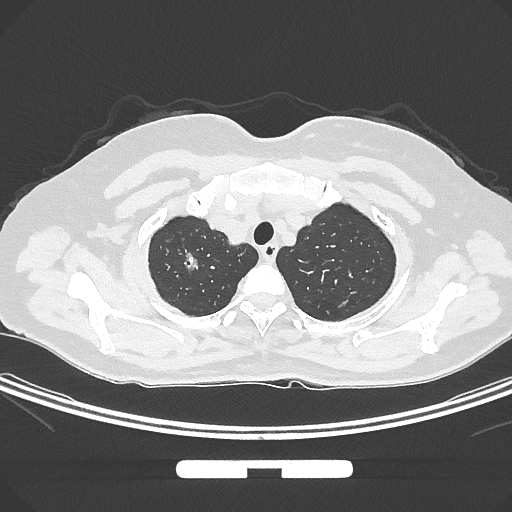
Chest CT, one axial slice. Slice 256 of 294 in the series (ordered by position). Lung window (W 1500 / L -600 HU). 1 mm slice thickness. 512 × 512 image matrix. Female patient, age 58 years. Case-level facts recorded for this patient, not image findings: clinical TNM (as recorded): T1b N0 M0; histopathological grade: G2-3.
Outlined on this slice (rectangle marked by the reading radiologist):
- lung tumour (recorded histology: adenocarcinoma): bounding box (x1, y1, x2, y2) in pixels: (174, 247, 205, 280)